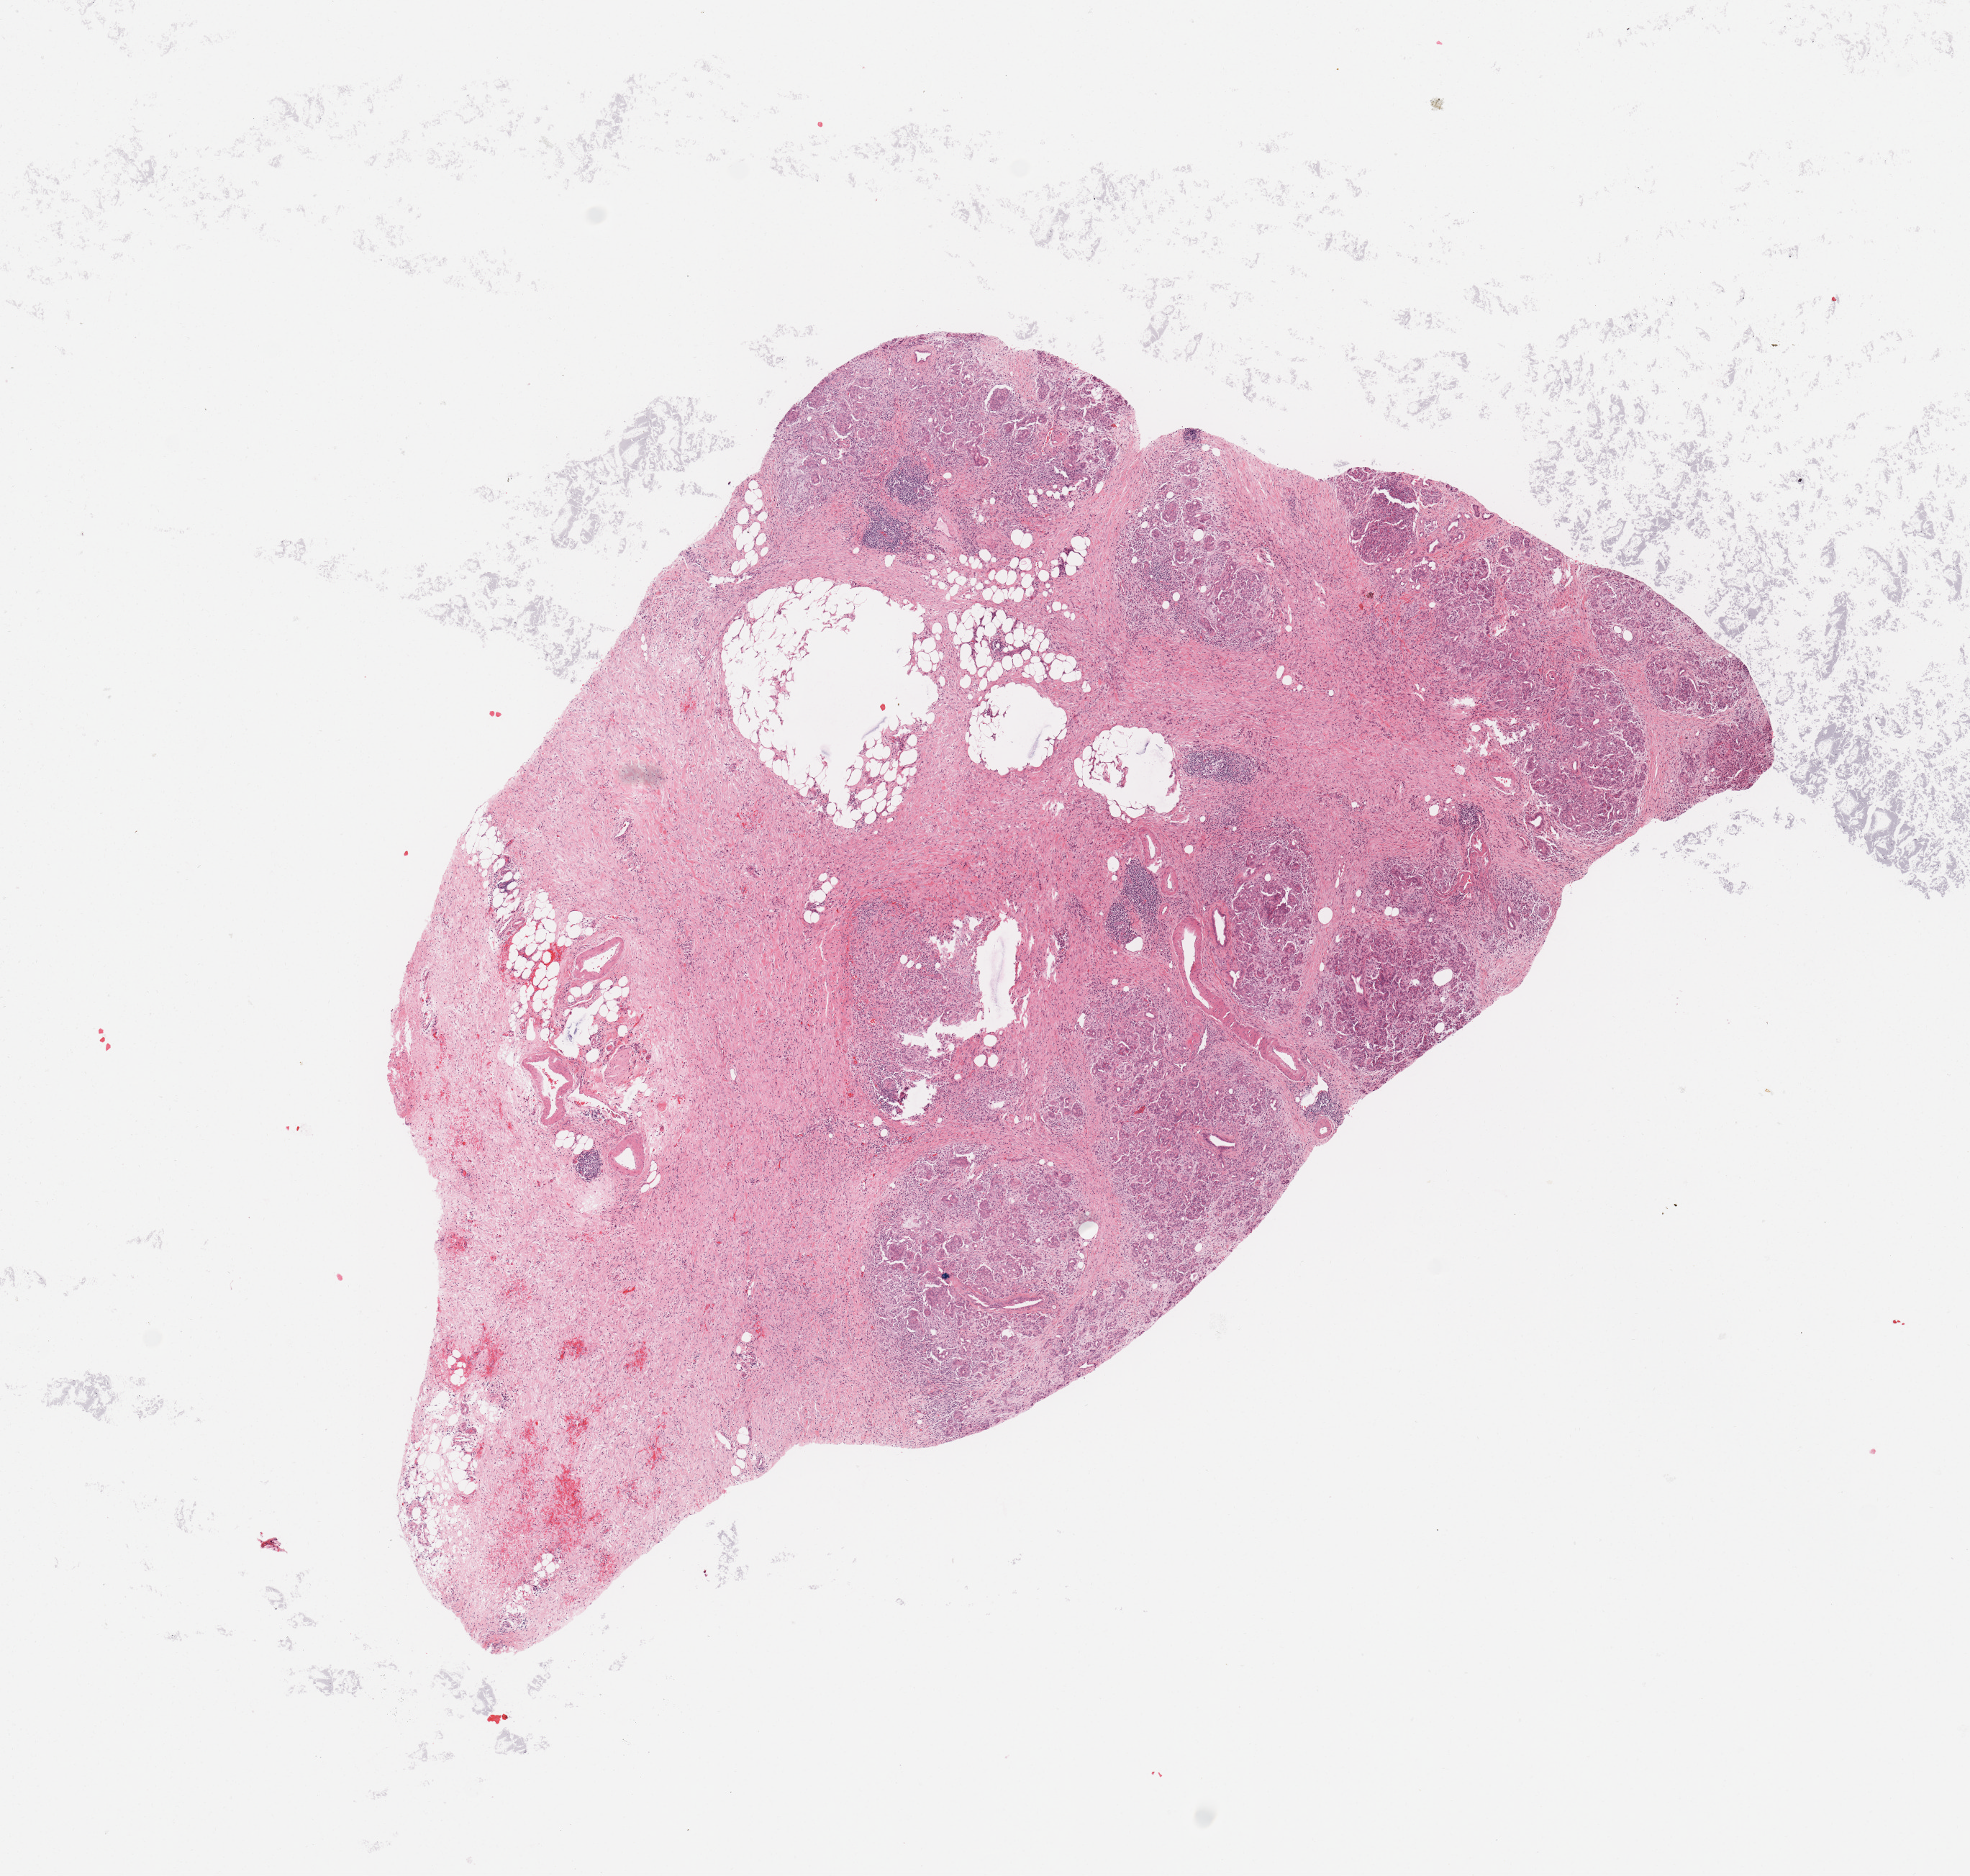
Digitized H&E-stained tissue section (whole slide) — a low-resolution overview of the entire scanned area, about 10.8 x 10.3 mm, normal (non-tumour) tissue sample, sampled site: pancreas. Male, 46 y/o.
This section: normal (non-tumour) tissue from the same patient. Patient diagnosis: Infiltrating duct carcinoma, NOS.